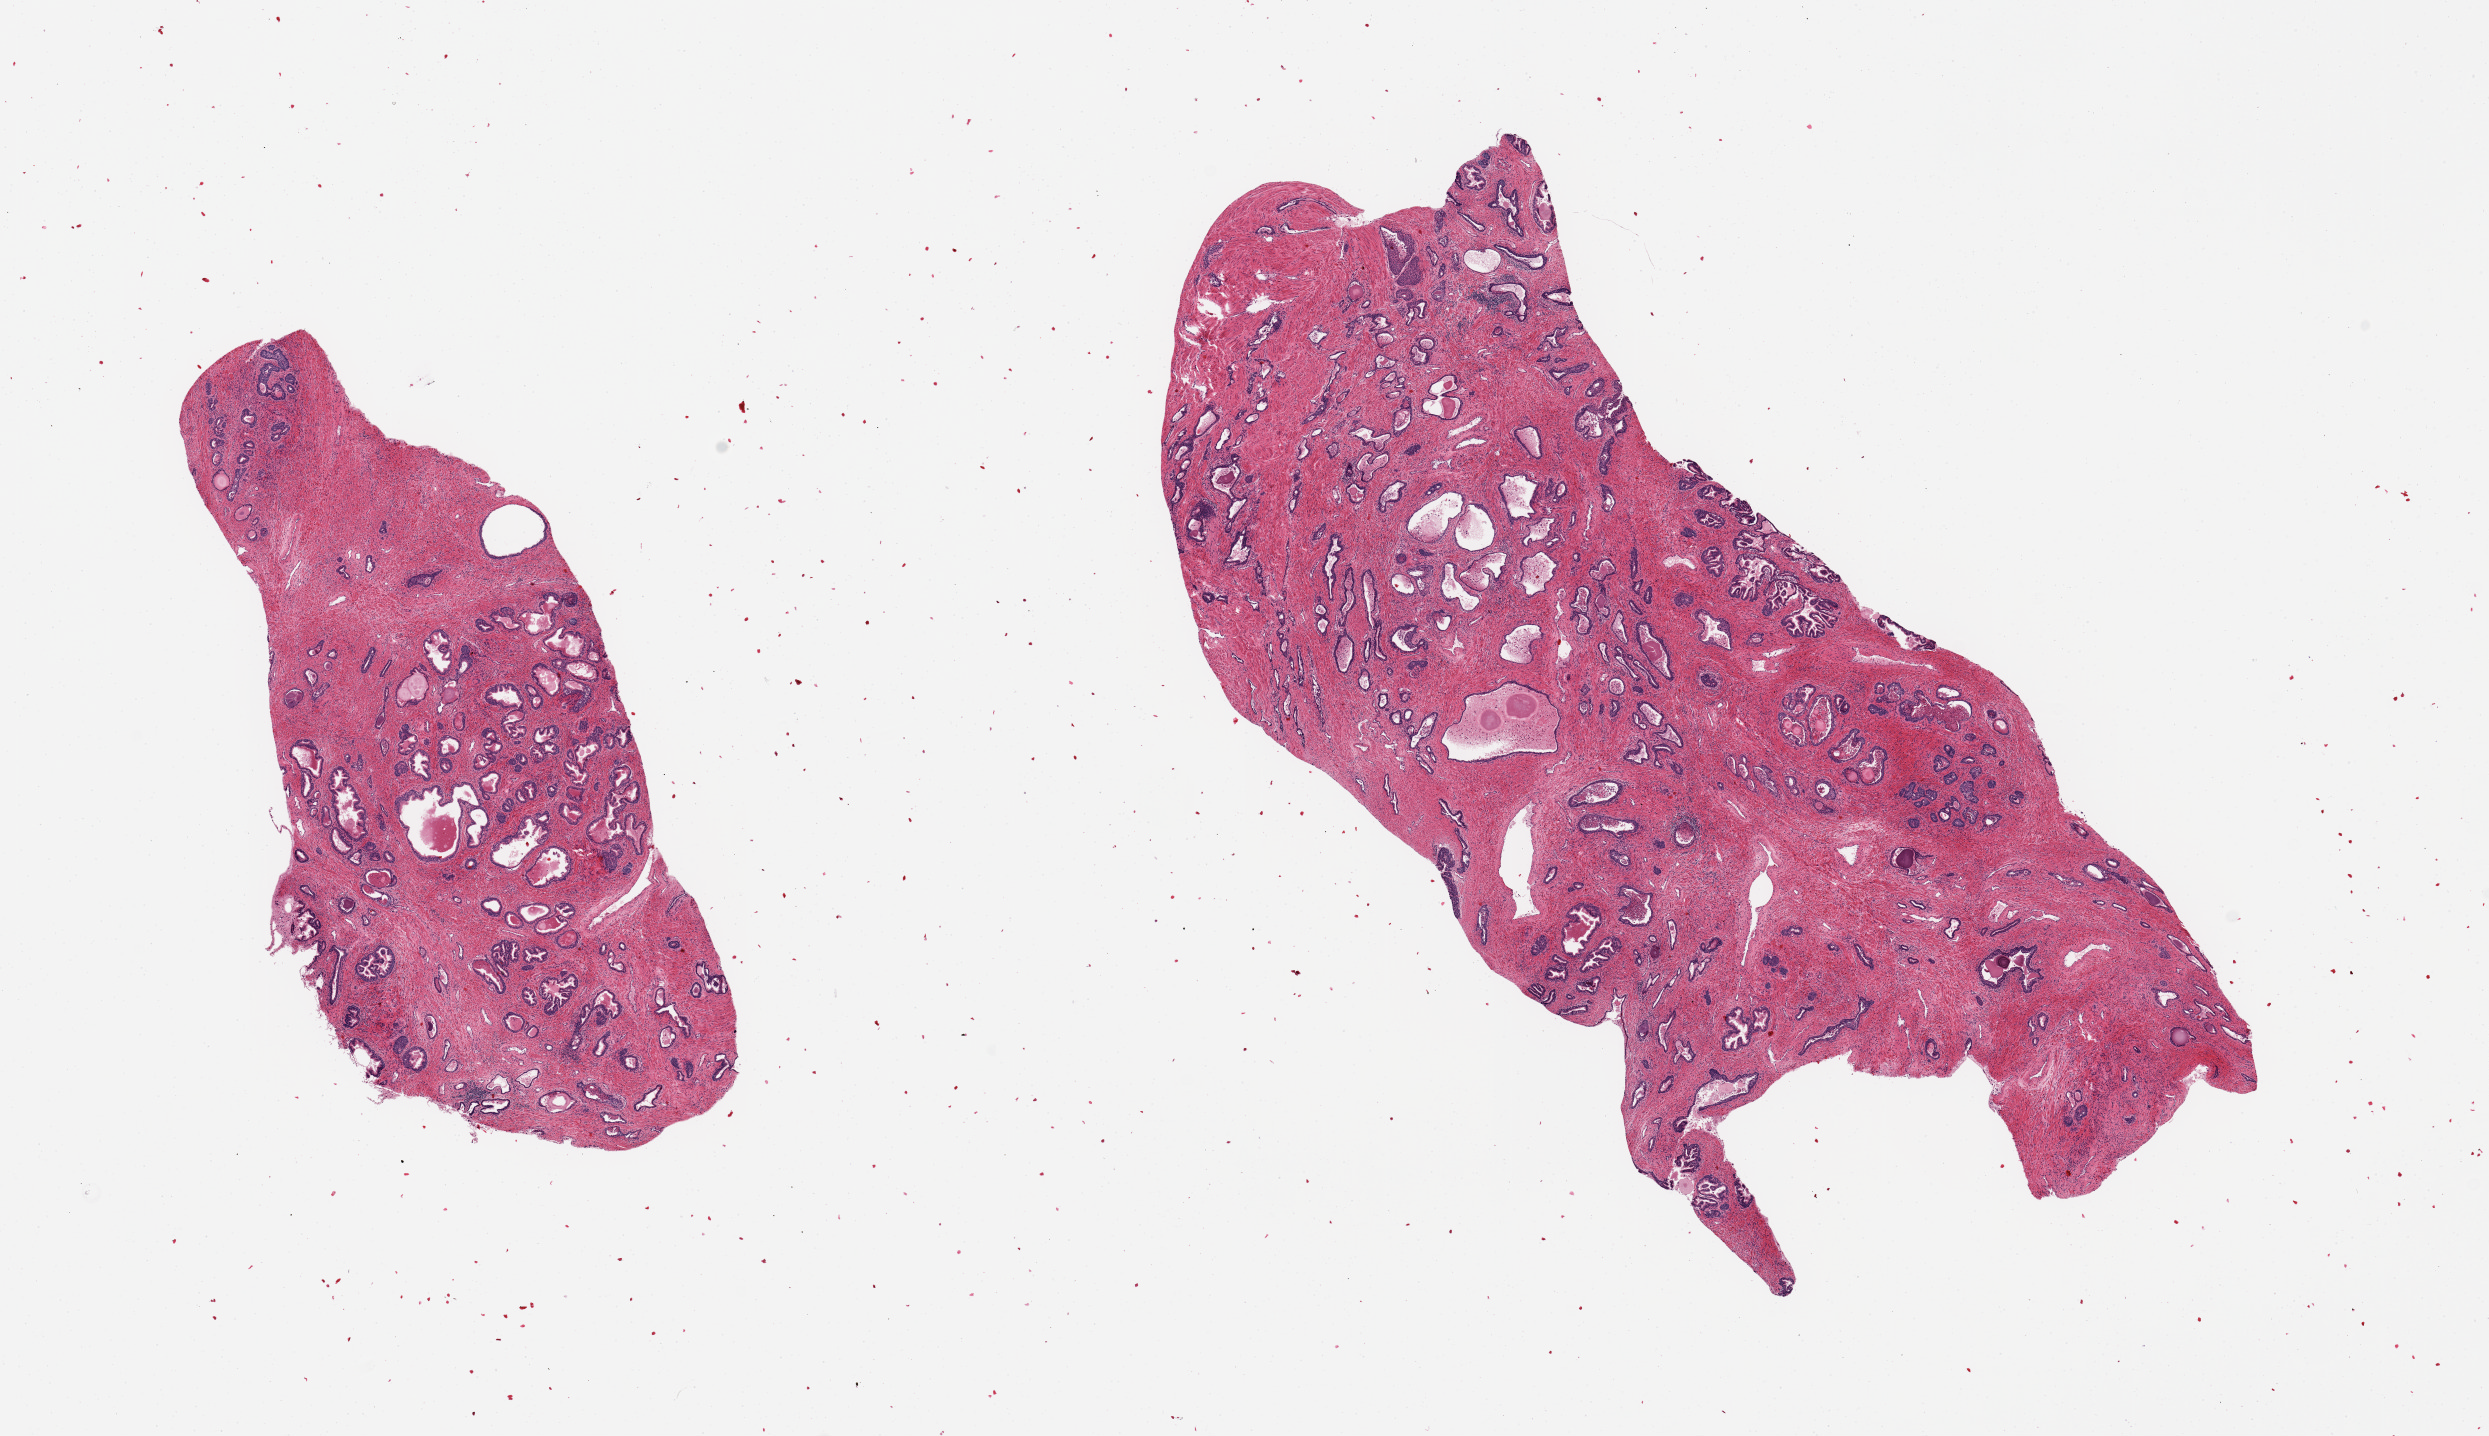
Haematoxylin and eosin whole-slide image, brightfield, low-resolution overview of the scanned area, about 19.7 x 11.4 mm; PAXgene-fixed, paraffin-embedded tissue; sampled site (target tissue): prostate; donor tissue sample.
Pathologist's review note for this sample: 2 pieces; minimal hyperplasia.